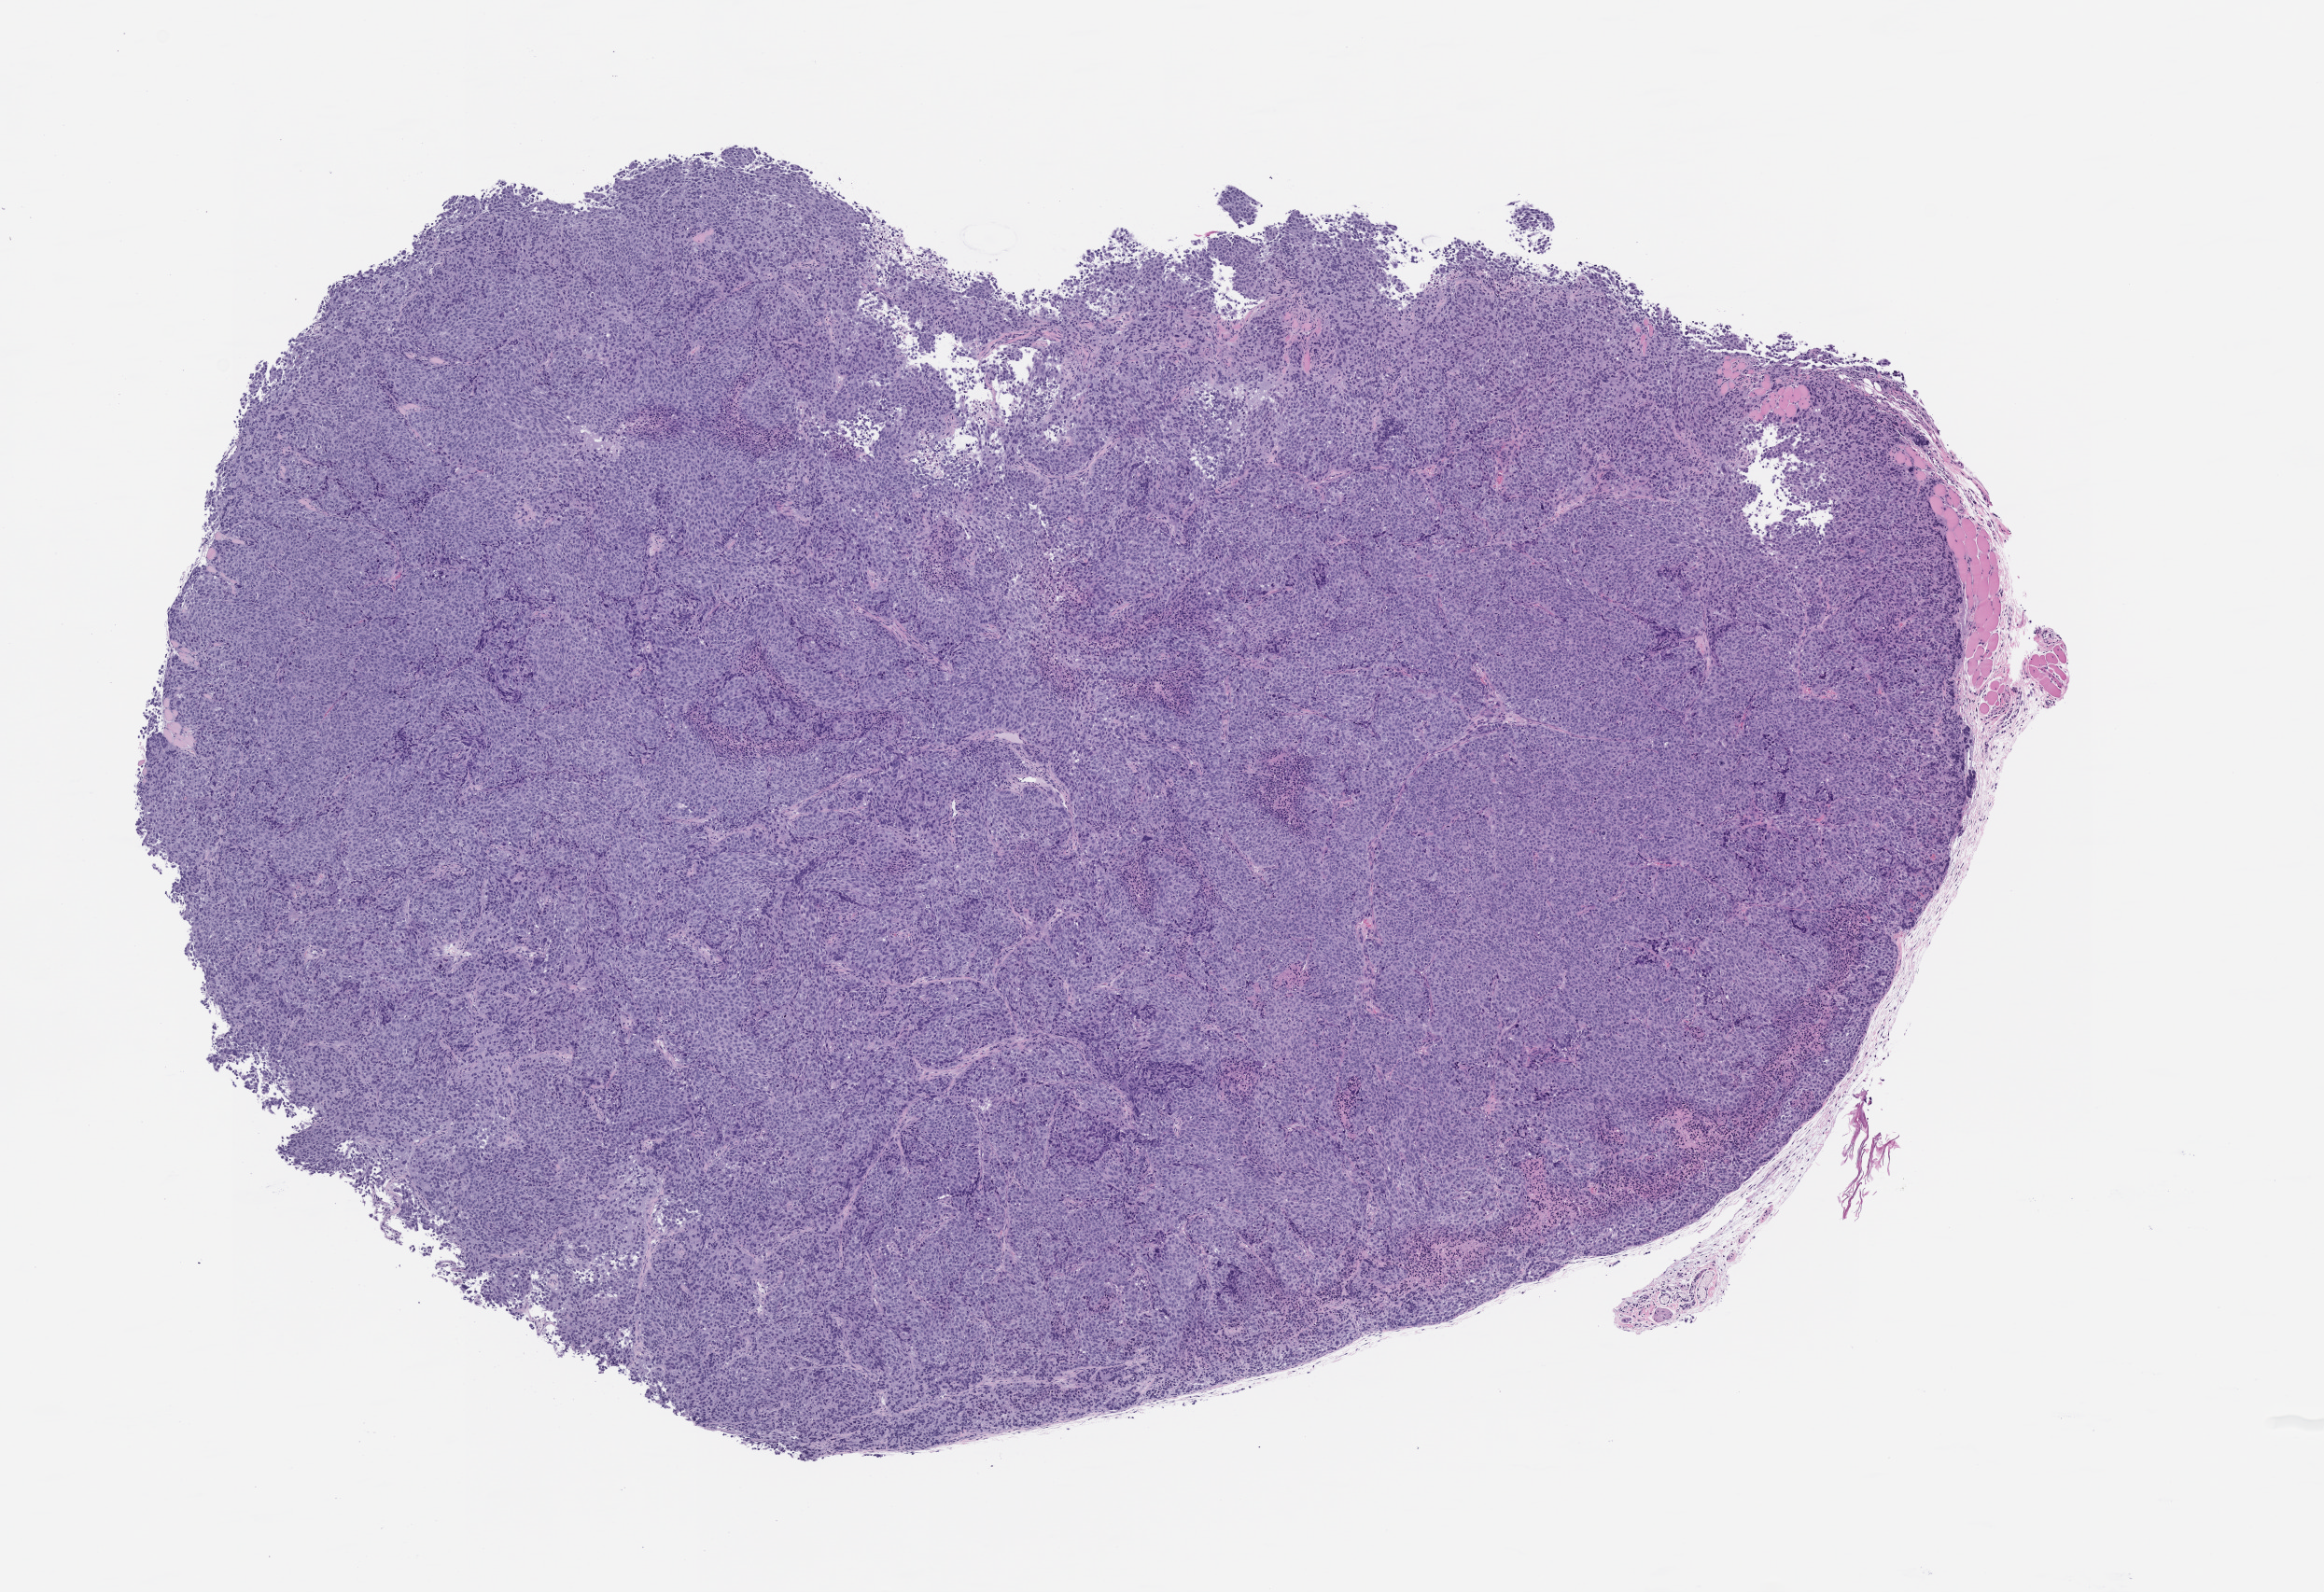
Hematoxylin and eosin (H&E) whole-slide image of a patient-derived xenograft (PDX) tumor grown in a mouse, passage 1 — low-resolution overview of the scanned area, about 10.0 x 6.9 mm. Formalin-fixed, paraffin-embedded (FFPE) tissue. Originating tumor site category: lung.
Originating patient diagnosis: Lung Squamous Cell Carcinoma.